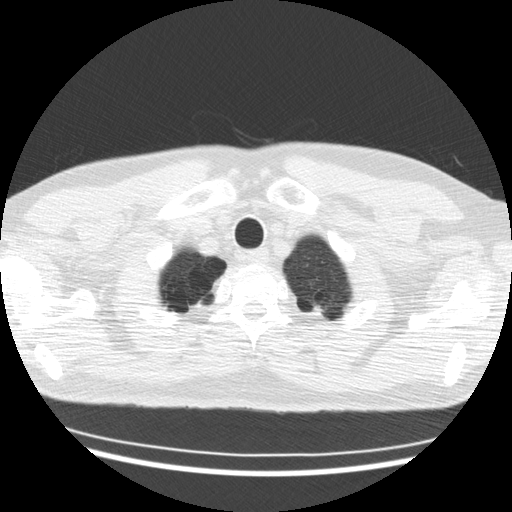
Low-dose screening chest CT, axial slice. Second screening round (one year after baseline). Lung window (W 1500 / L -600 HU). Slice 17 of 176 in the series. 512 × 512 image matrix. Male, age 57 years at enrolment. Former smoker at enrolment.
- Expert-annotated lung lesion, bounding box <303,298,333,324> (left, top, right, bottom; pixels).
- The screening reader recorded 2 non-calcified nodules or masses ≥4 mm on this exam; which of them this box marks is not recorded.
- Lung cancer was diagnosed 332 days after this screen: adenocarcinoma, NOS, left upper lobe, stage IV (AJCC 6th edition), 50 mm at pathology.